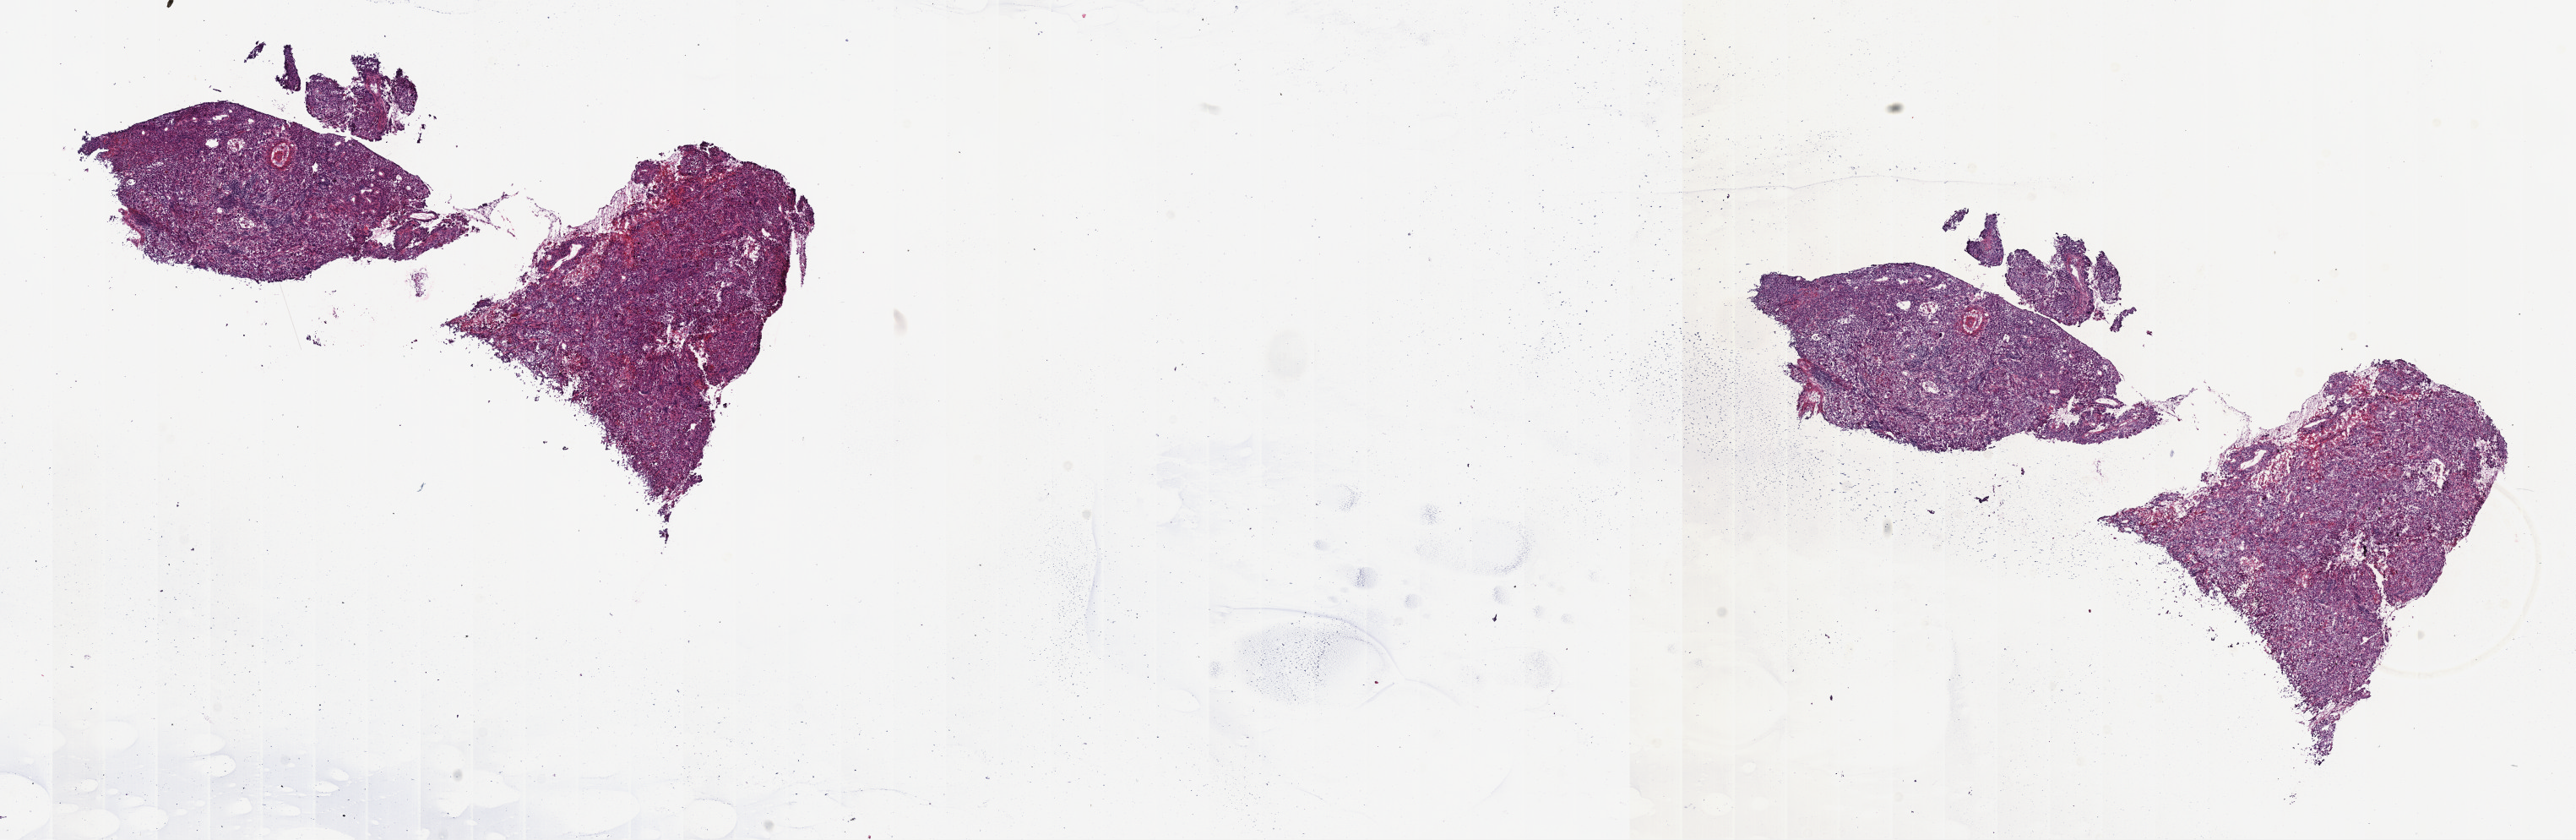
Whole-slide histology image, H&E — whole scanned area (about 24.7 x 8.0 mm, from a 40x scan) shown as a low-resolution overview. Frozen section from the top of the tissue portion. Cervix, primary tumour sample. Patient: female, age at initial diagnosis 28 years. Histologic grade: G3 (poorly differentiated). Pathologist review of this section (percent, as recorded): tumour cells 70%, tumour nuclei 70%, normal cells 10%, stromal cells 10%, necrosis 10%. Inflammatory infiltration, as recorded: lymphocyte infiltration 10%, monocyte infiltration 0%, neutrophil infiltration 0%.
• histologic diagnosis: Squamous cell carcinoma, NOS (cervix uteri)
• FIGO stage: IIA